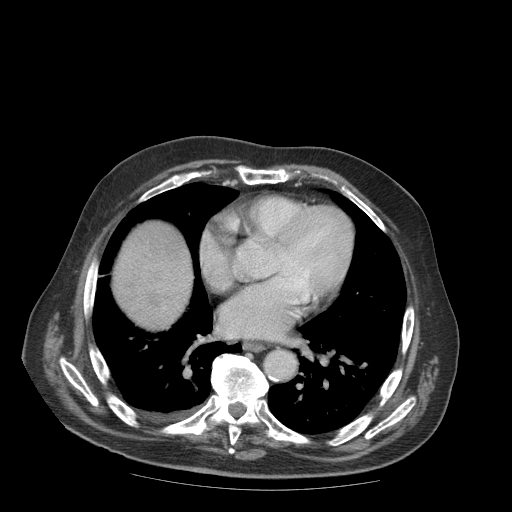
Contrast-enhanced abdominal CT (liver protocol), one axial slice; slice 93 of 99 in the series (ordered by position); soft-tissue window (W 400 / L 40 HU); 2.5 mm slice thickness; 512 × 512 image matrix, field of view 420 × 420 mm. From the clinical record (not read from this slice): diagnosis: hepatocellular carcinoma (patient treated with transarterial chemoembolisation; whether this scan precedes or follows treatment is not stated here); TNM stage (as recorded): Stage-IIIB; Child-Pugh class: A.
Outlined on this slice (semi-automatic segmentation, software-assisted and operator-edited):
- abdominal aorta: box from (x=266, y=349) to (x=296, y=379) px
- liver parenchyma outside the tumour (the mass and vessels are separate outlines, so this box may not span the whole liver): (x=112, y=220)–(x=192, y=326)